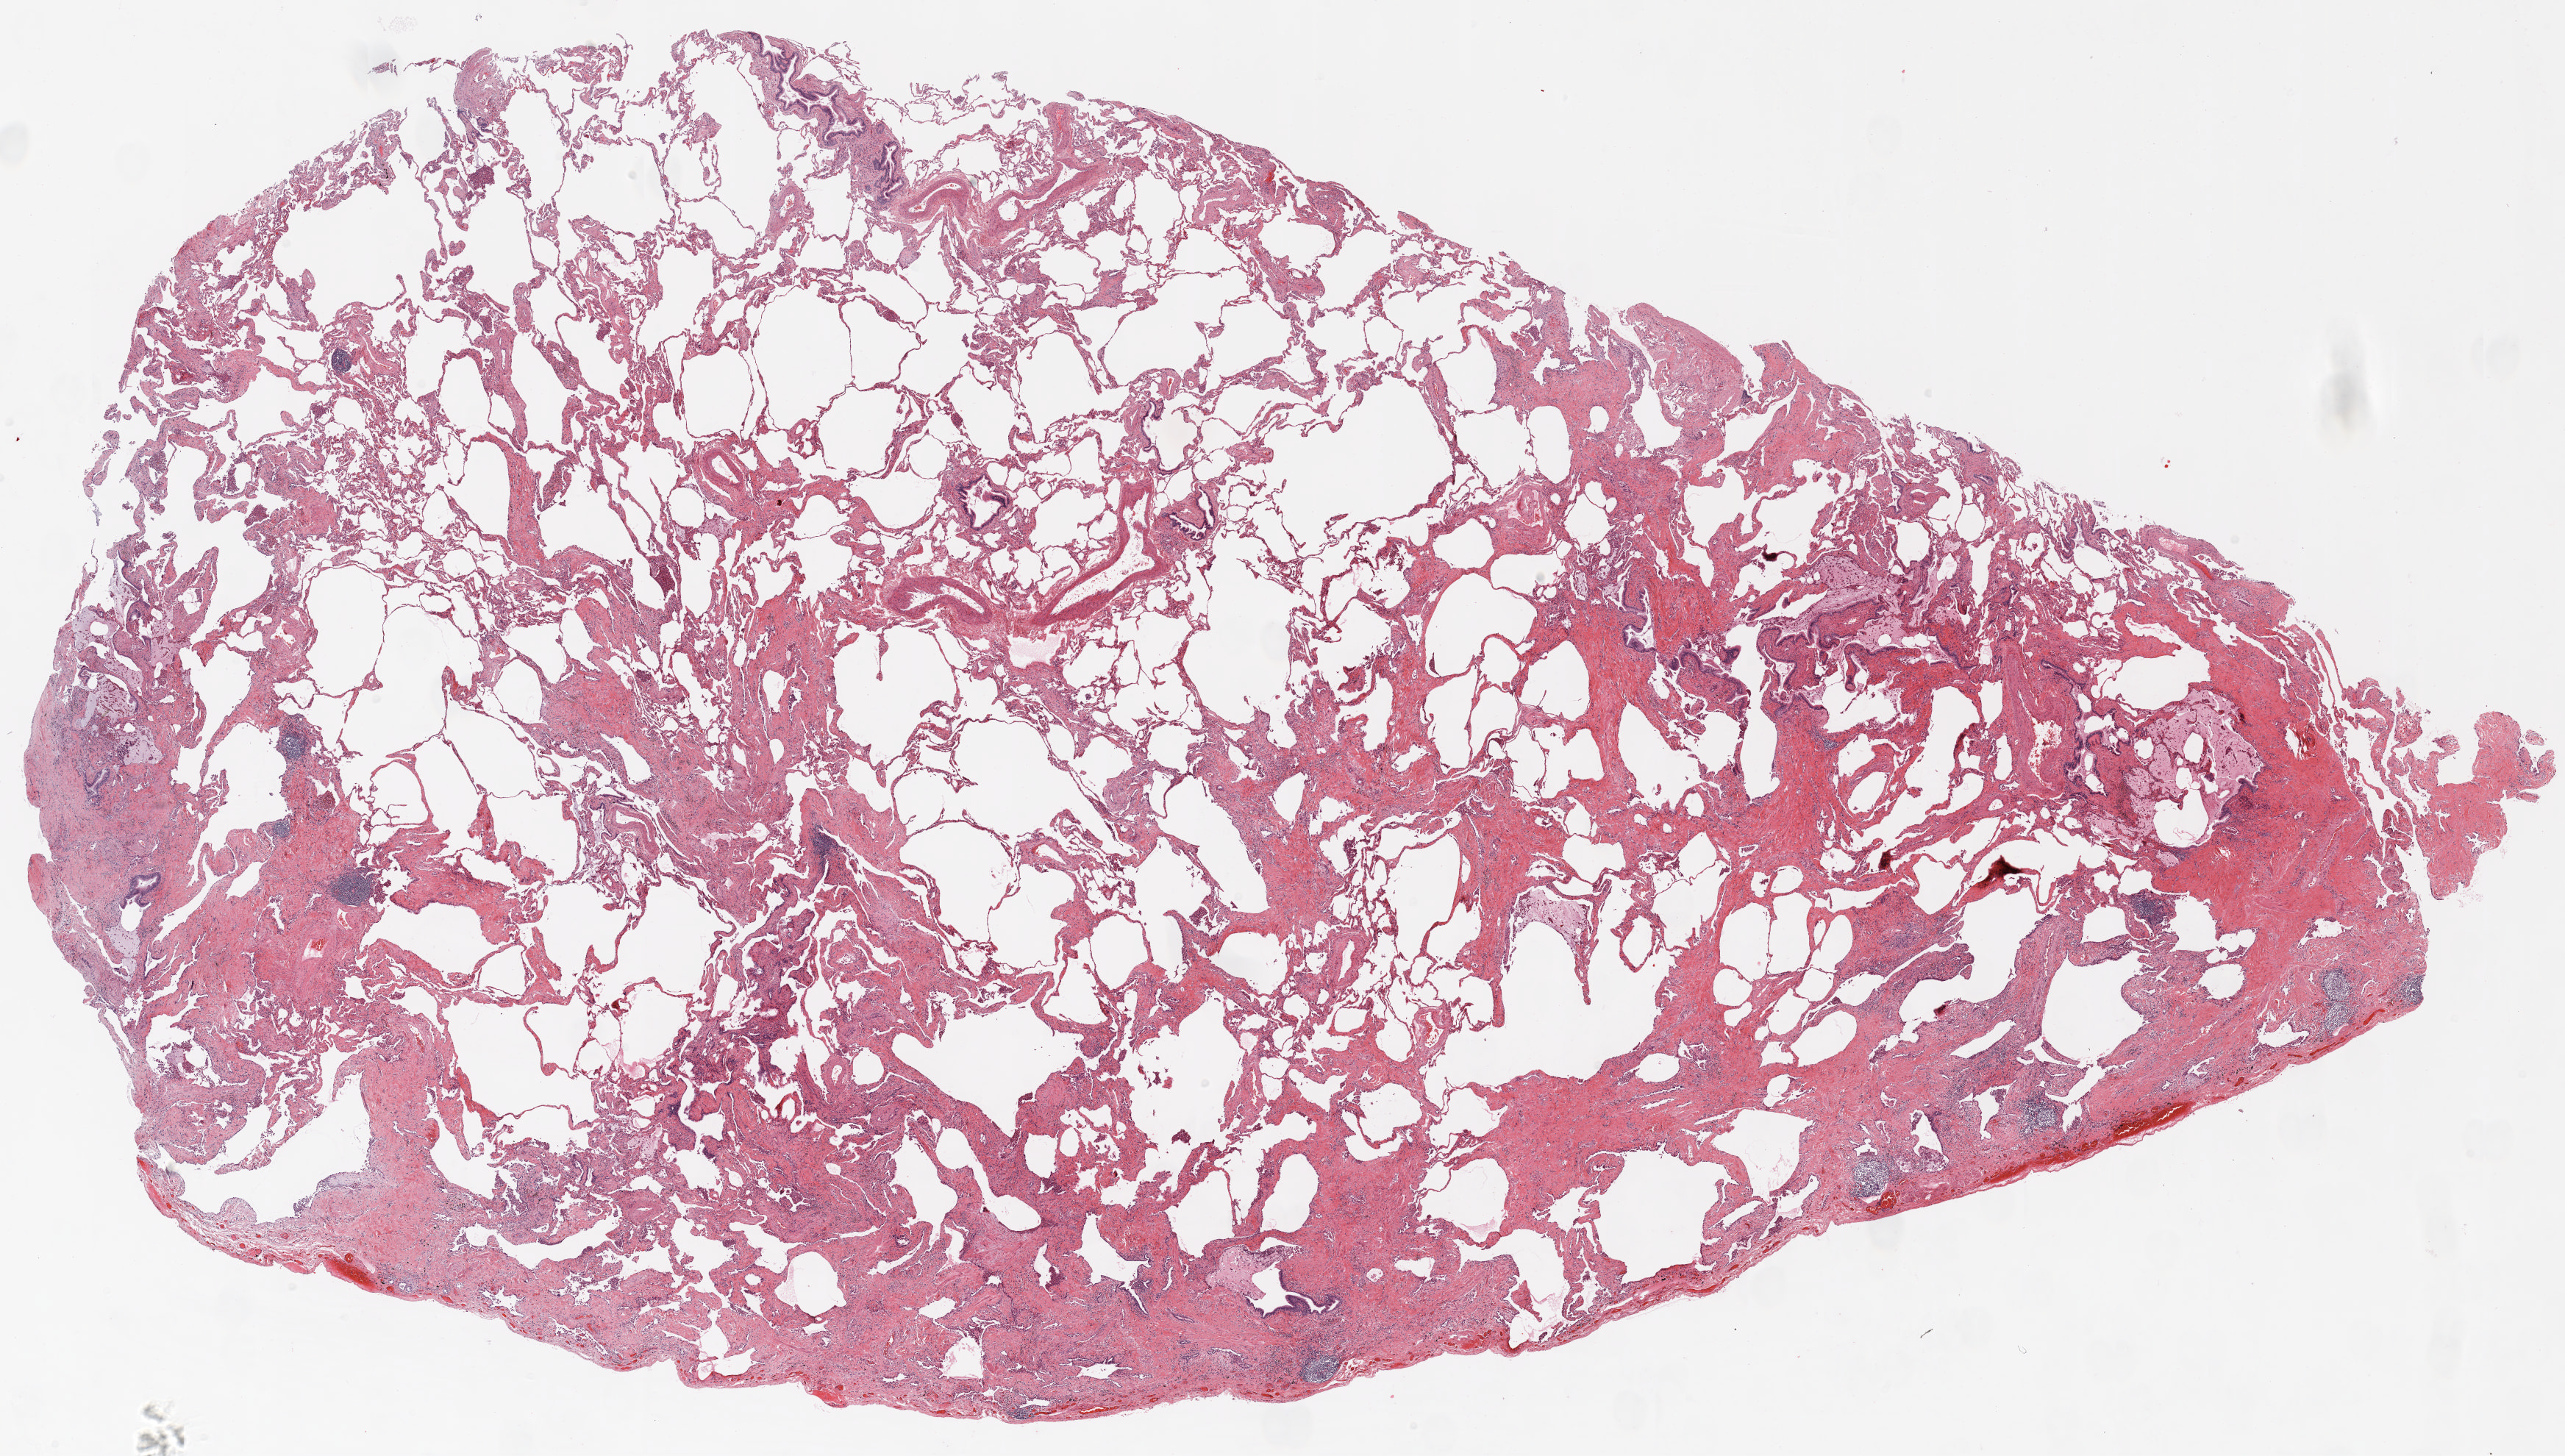
H&E-stained whole-slide image — whole scanned area (about 28.0 x 15.9 mm, slide scanned at 20x) shown as a low-resolution overview, formalin-fixed paraffin-embedded (FFPE) section, lung. Male patient, aged 66 at enrolment. Grade: poorly differentiated (G3).
Primary tumour location (clinical record): right upper lobe. Tumour size (pathology): 23 mm. Stage (AJCC 6th edition): IB. Participant's lung-cancer diagnosis: Squamous cell carcinoma, NOS. Note: participant had 2 primary lung cancers recorded; fields above describe the first.